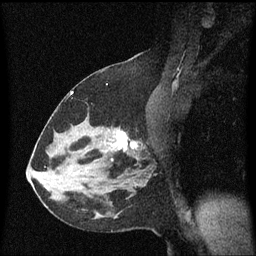
Breast MRI (dynamic contrast-enhanced), one sagittal slice. Position 35 of 60 along the scan axis. Dynamic contrast-enhanced series, image 2 of 3 at this slice position (ordered by acquisition). 1.5 T. TE 4.2 ms, TR 8.4 ms. 256 × 256 image matrix. Patient: female, 37 years. Case-level facts recorded for this patient, not image findings: setting: breast cancer imaged before/during neoadjuvant chemotherapy; receptor status: HR-positive, HER2-negative.
Outlined on this slice (semi-automatic segmentation, software-assisted and operator-edited):
- analysis volume of interest (the breast-tissue region the enhancement analysis was run in; not a lesion): bounding box (x1, y1, x2, y2) in pixels: (95, 108, 154, 171)
- tumour enhancement mask (voxels above the 70 % enhancement threshold inside the analysis volume of interest): (117, 132, 139, 151)